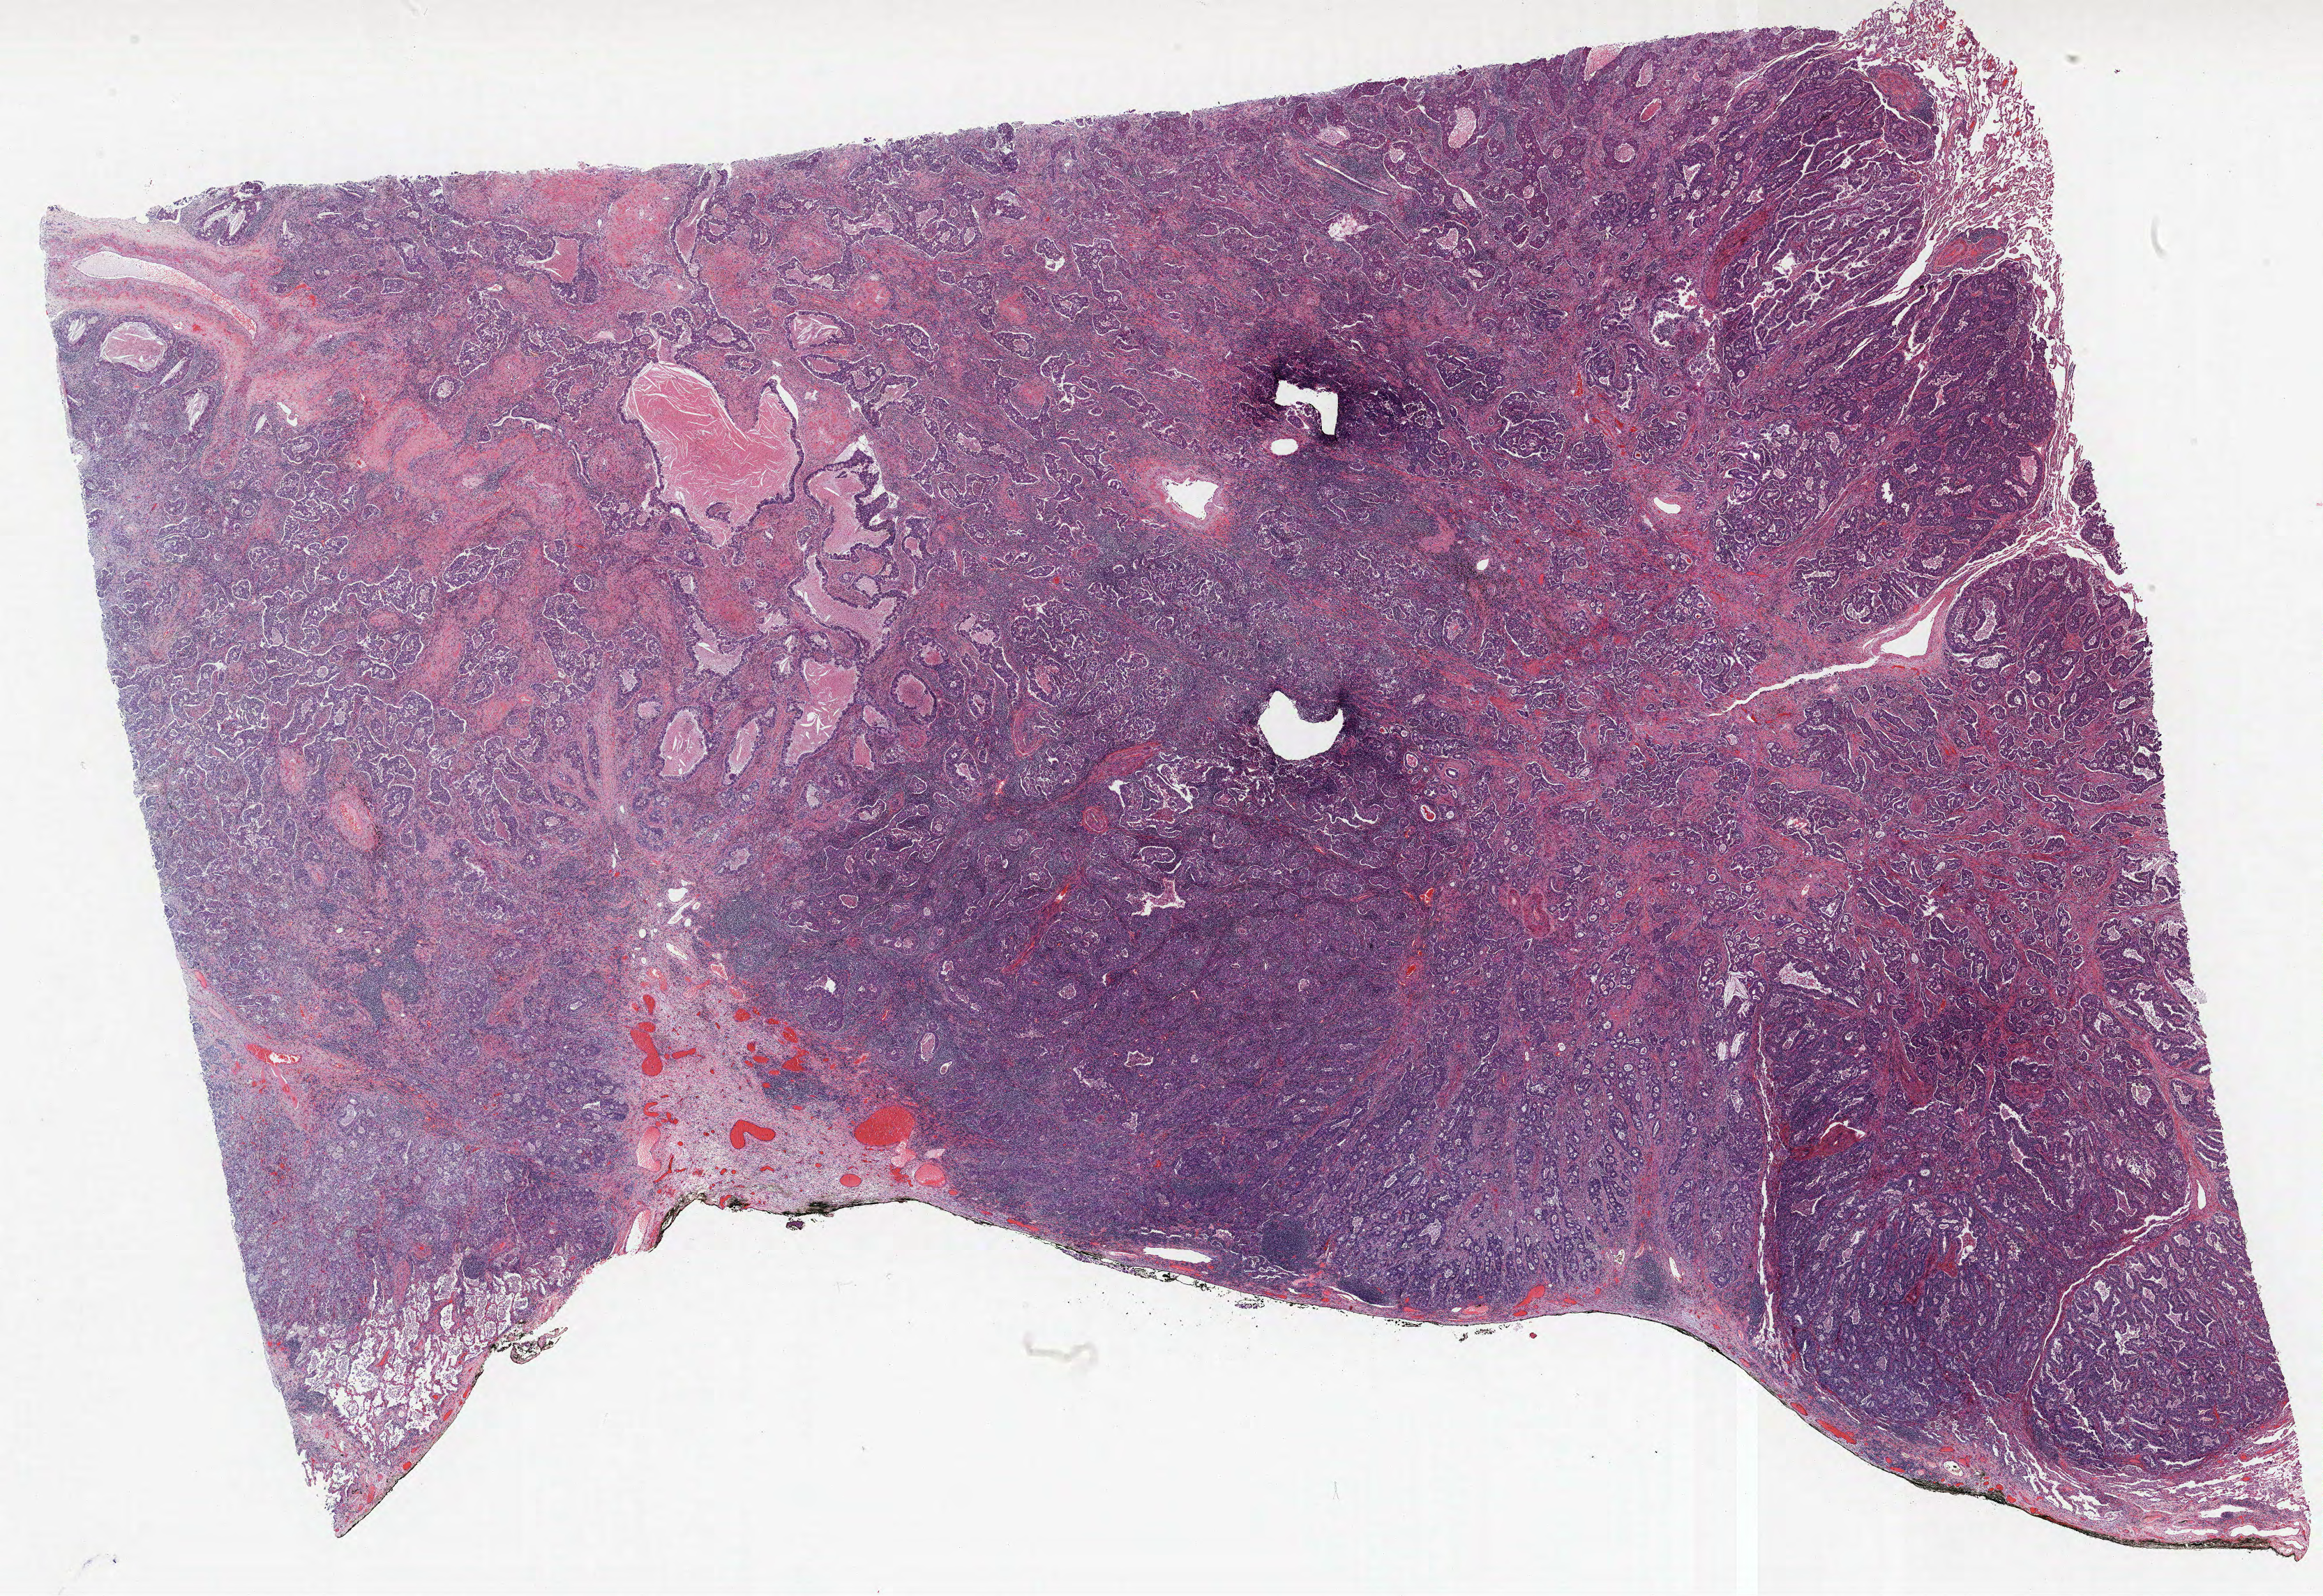
Whole-slide histology image, H&E-stained, low-resolution overview of the scanned area, about 26.6 x 18.3 mm (slide scanned at 40x); FFPE section; lung tissue. Female patient, aged 66 at enrolment. Former smoker at enrolment. Grade: moderately differentiated (G2).
• primary tumour location (clinical record): right lower lobe
• stage (AJCC 6th edition): IV
• tumour size (pathology): 60 mm
• ICD-O-3 topography: lower lobe of lung (C34.3)
• participant's lung-cancer diagnosis: Adenocarcinoma, NOS